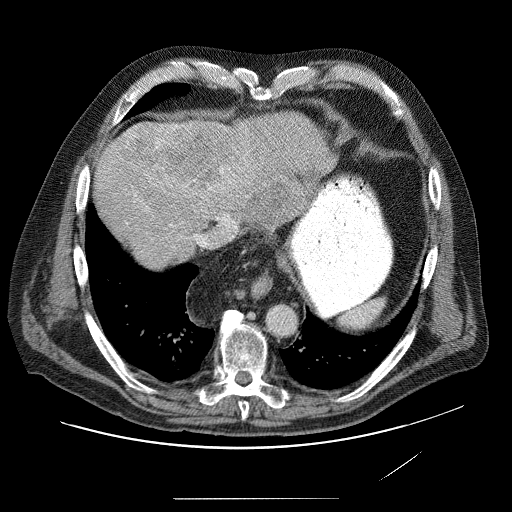
Contrast-enhanced abdominal CT (liver protocol), one axial slice; position 71 of 89 along the scan axis; reconstruction kernel STANDARD; 120 kVp; soft-tissue window (W 400 / L 40 HU); 2.5 mm slice thickness; 512 × 512 image matrix, field of view 420 × 420 mm. Case-level facts recorded for this patient, not image findings: diagnosis: hepatocellular carcinoma (patient treated with transarterial chemoembolisation; whether this scan precedes or follows treatment is not stated here); TNM stage (as recorded): Stage-IVA; Child-Pugh class: A; tumour differentiation: moderately differentiated; tumour nodularity: multinodular.
Annotated regions visible in this slice (semi-automatically segmented with operator editing):
- liver parenchyma outside the tumour (the mass and vessels are separate outlines, so this box may not span the whole liver): bounding box [x1, y1, x2, y2] px = [96, 118, 312, 248]
- mass: [119, 117, 307, 219]
- liver vessels: [113, 169, 223, 245]